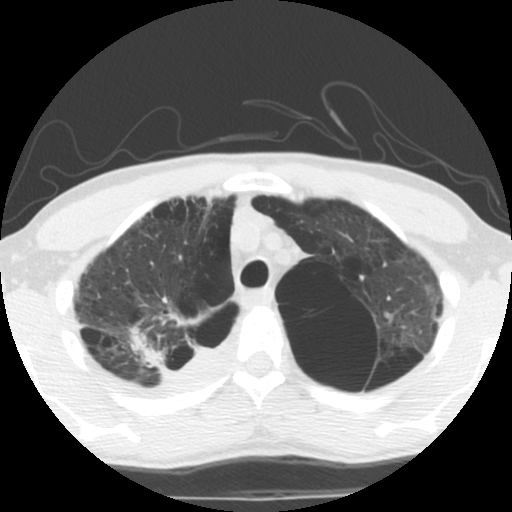
Low-dose screening chest CT, axial slice; second annual screen; lung window (W 1500 / L -600 HU); 2.5 mm slice thickness; standard (soft-tissue) reconstruction kernel (STANDARD); 512 × 512 image matrix, field of view 295 × 295 mm. Male participant, aged 62 years at enrolment. Current smoker at enrolment.
• Lesion marked by an expert reader, bounding box [x1, y1, x2, y2] px = [123, 319, 213, 391].
• Screening reader's record for this exam (one nodule recorded; not confirmed to be the boxed lesion): non-calcified nodule or mass ≥4 mm, 35 × 25 mm, soft tissue attenuation.
• Later outcome: lung cancer diagnosed 14 days after this screen — non-small cell carcinoma, right upper lobe, poorly differentiated (G3), stage IA (AJCC 6th edition), 70 mm at pathology.